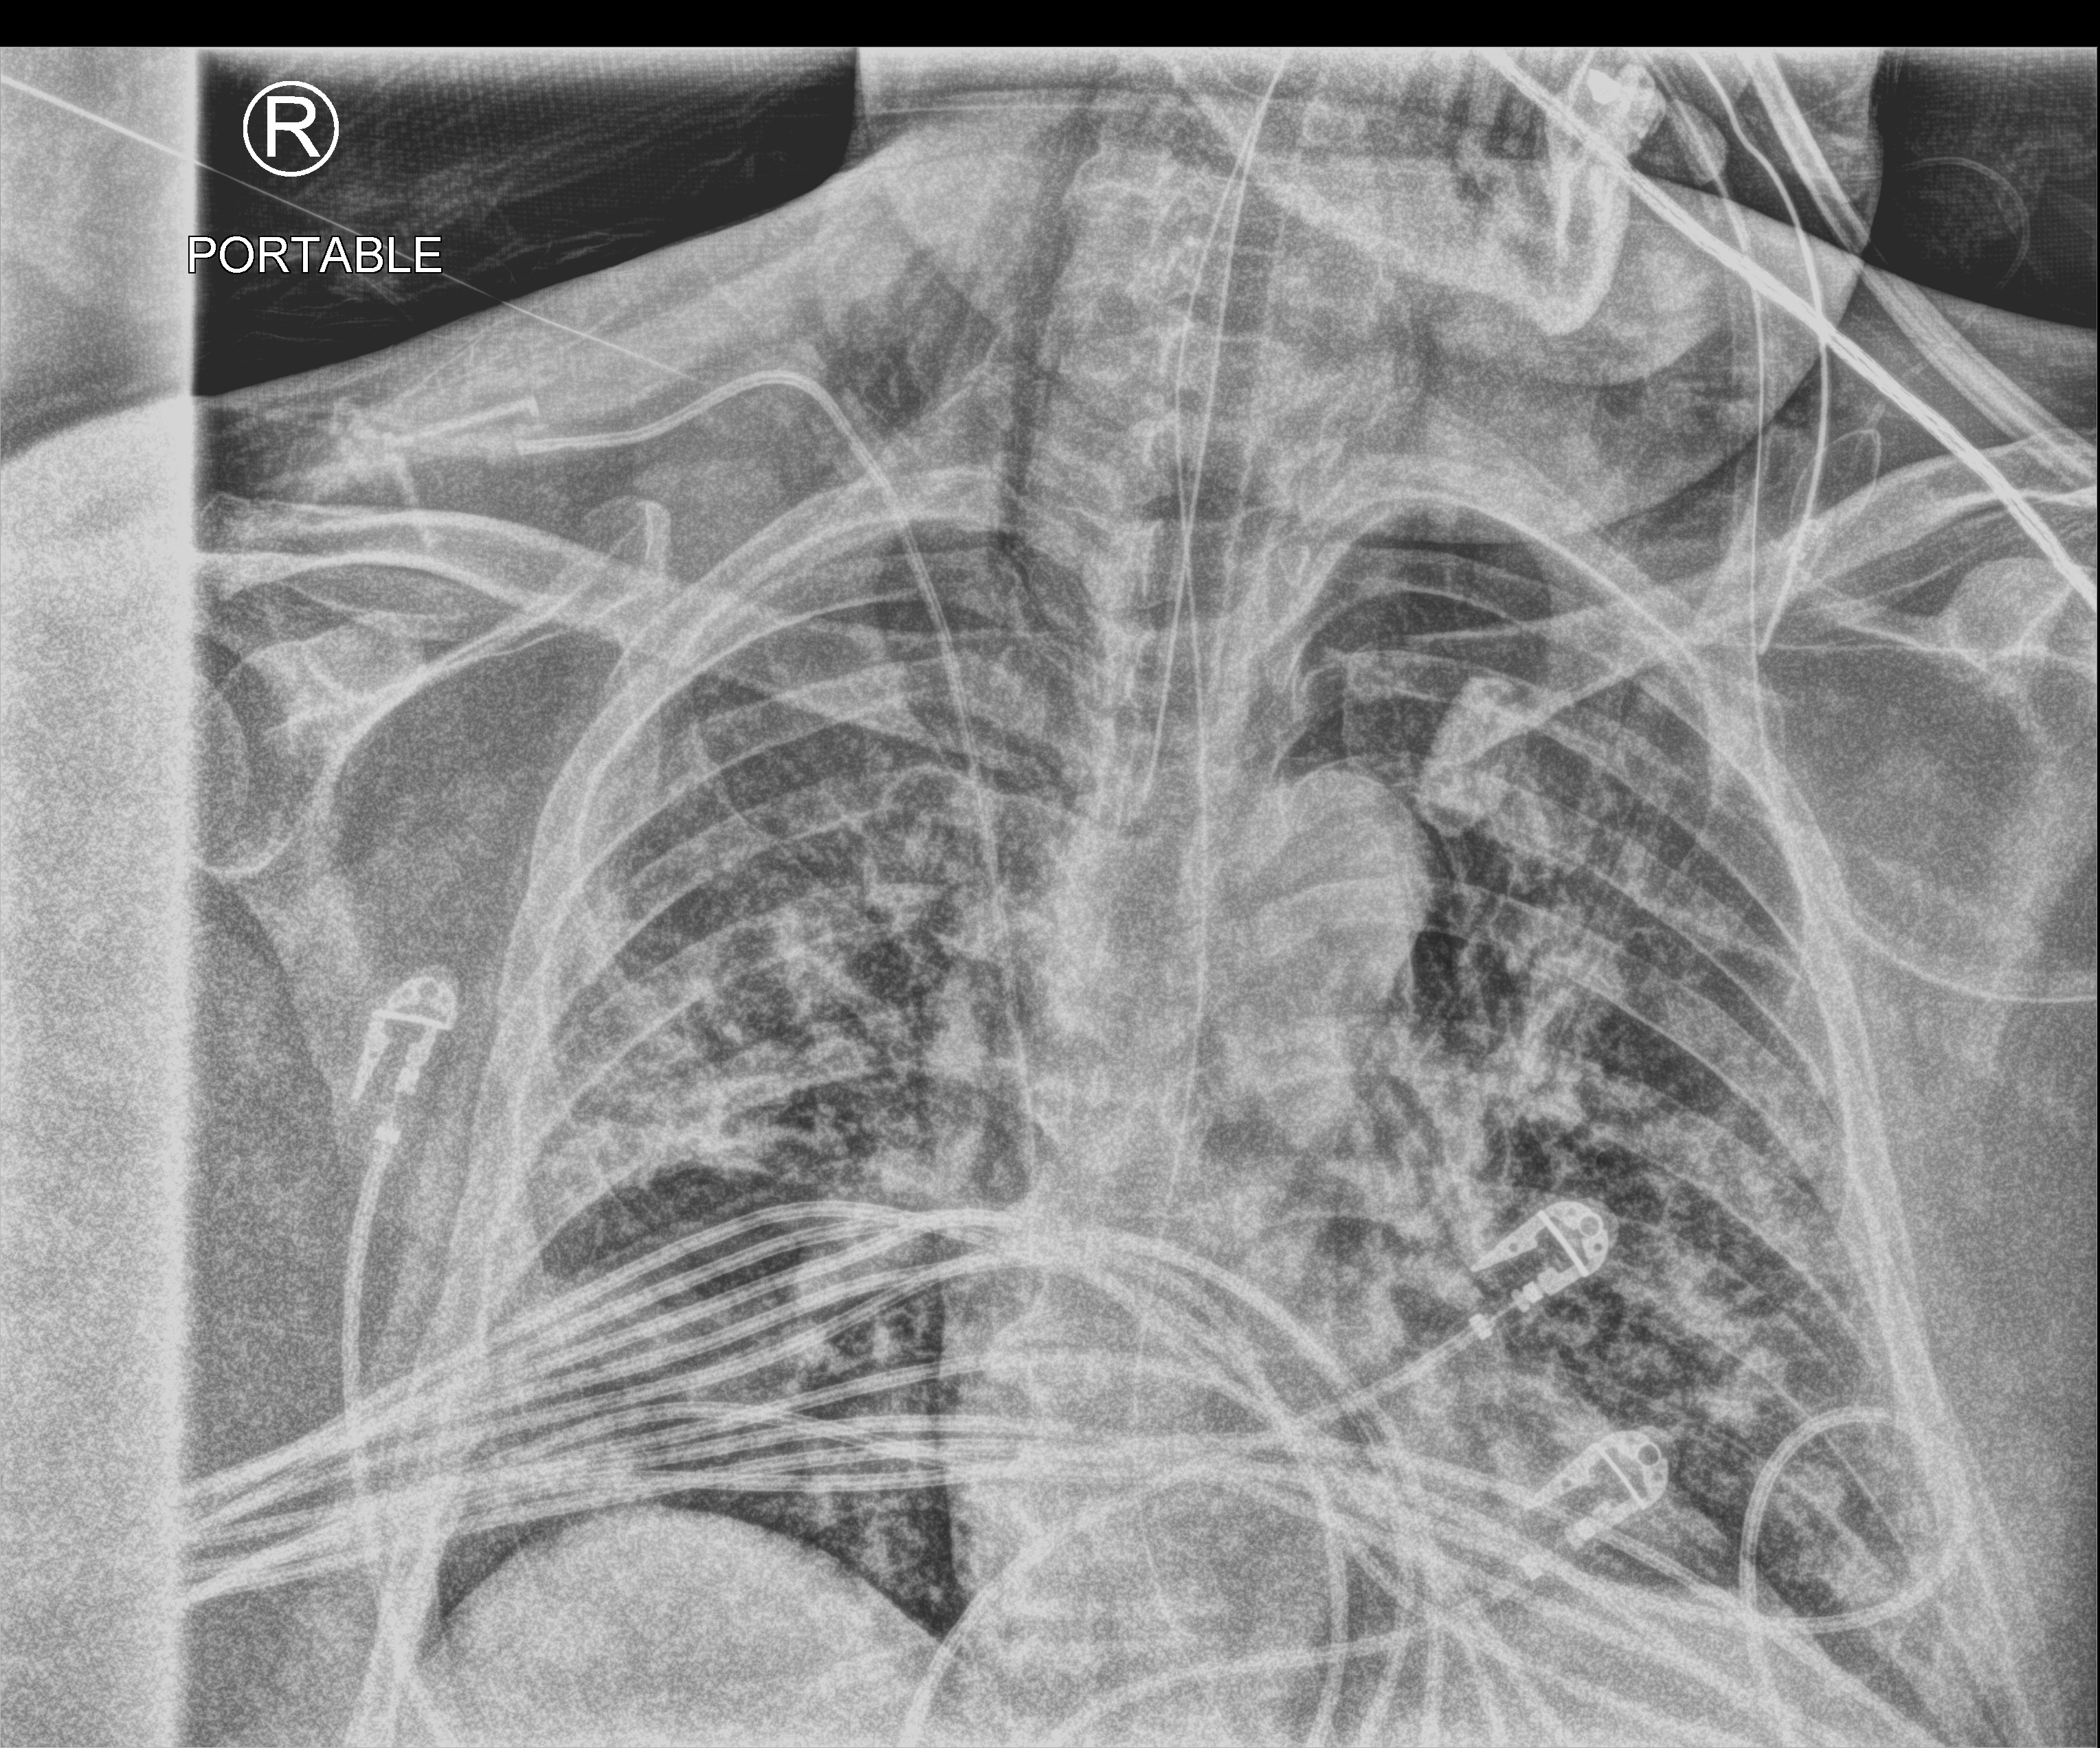
Chest X-ray (portable); anteroposterior (AP) projection. Patient hospitalised with COVID-19, aged 18–59 years.
From the hospital-stay record, not from the radiograph (when in the stay this image was taken is not recorded):
- admitted to intensive care during this hospital stay: yes
- diabetes (admission record): no
- hypertension (admission record): yes